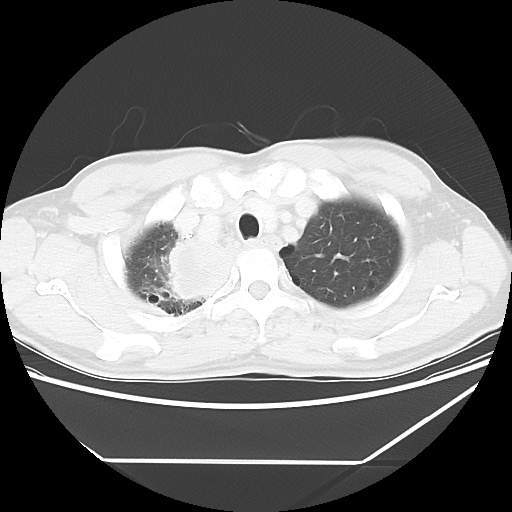
Chest CT, one axial slice. Slice 52 of 60 in the series (ordered by position). 120 kVp. Lung window (W 1500 / L -600 HU). 512 × 512 image matrix, field of view 367 × 367 mm. Male patient, age 58 years. From the clinical record (not read from this slice): clinical TNM (as recorded): T2 N2 M0.
Structures marked on this image (rectangle marked by the reading radiologist):
- lung tumour (recorded histology: squamous cell carcinoma): box from (x=154, y=233) to (x=236, y=312) px